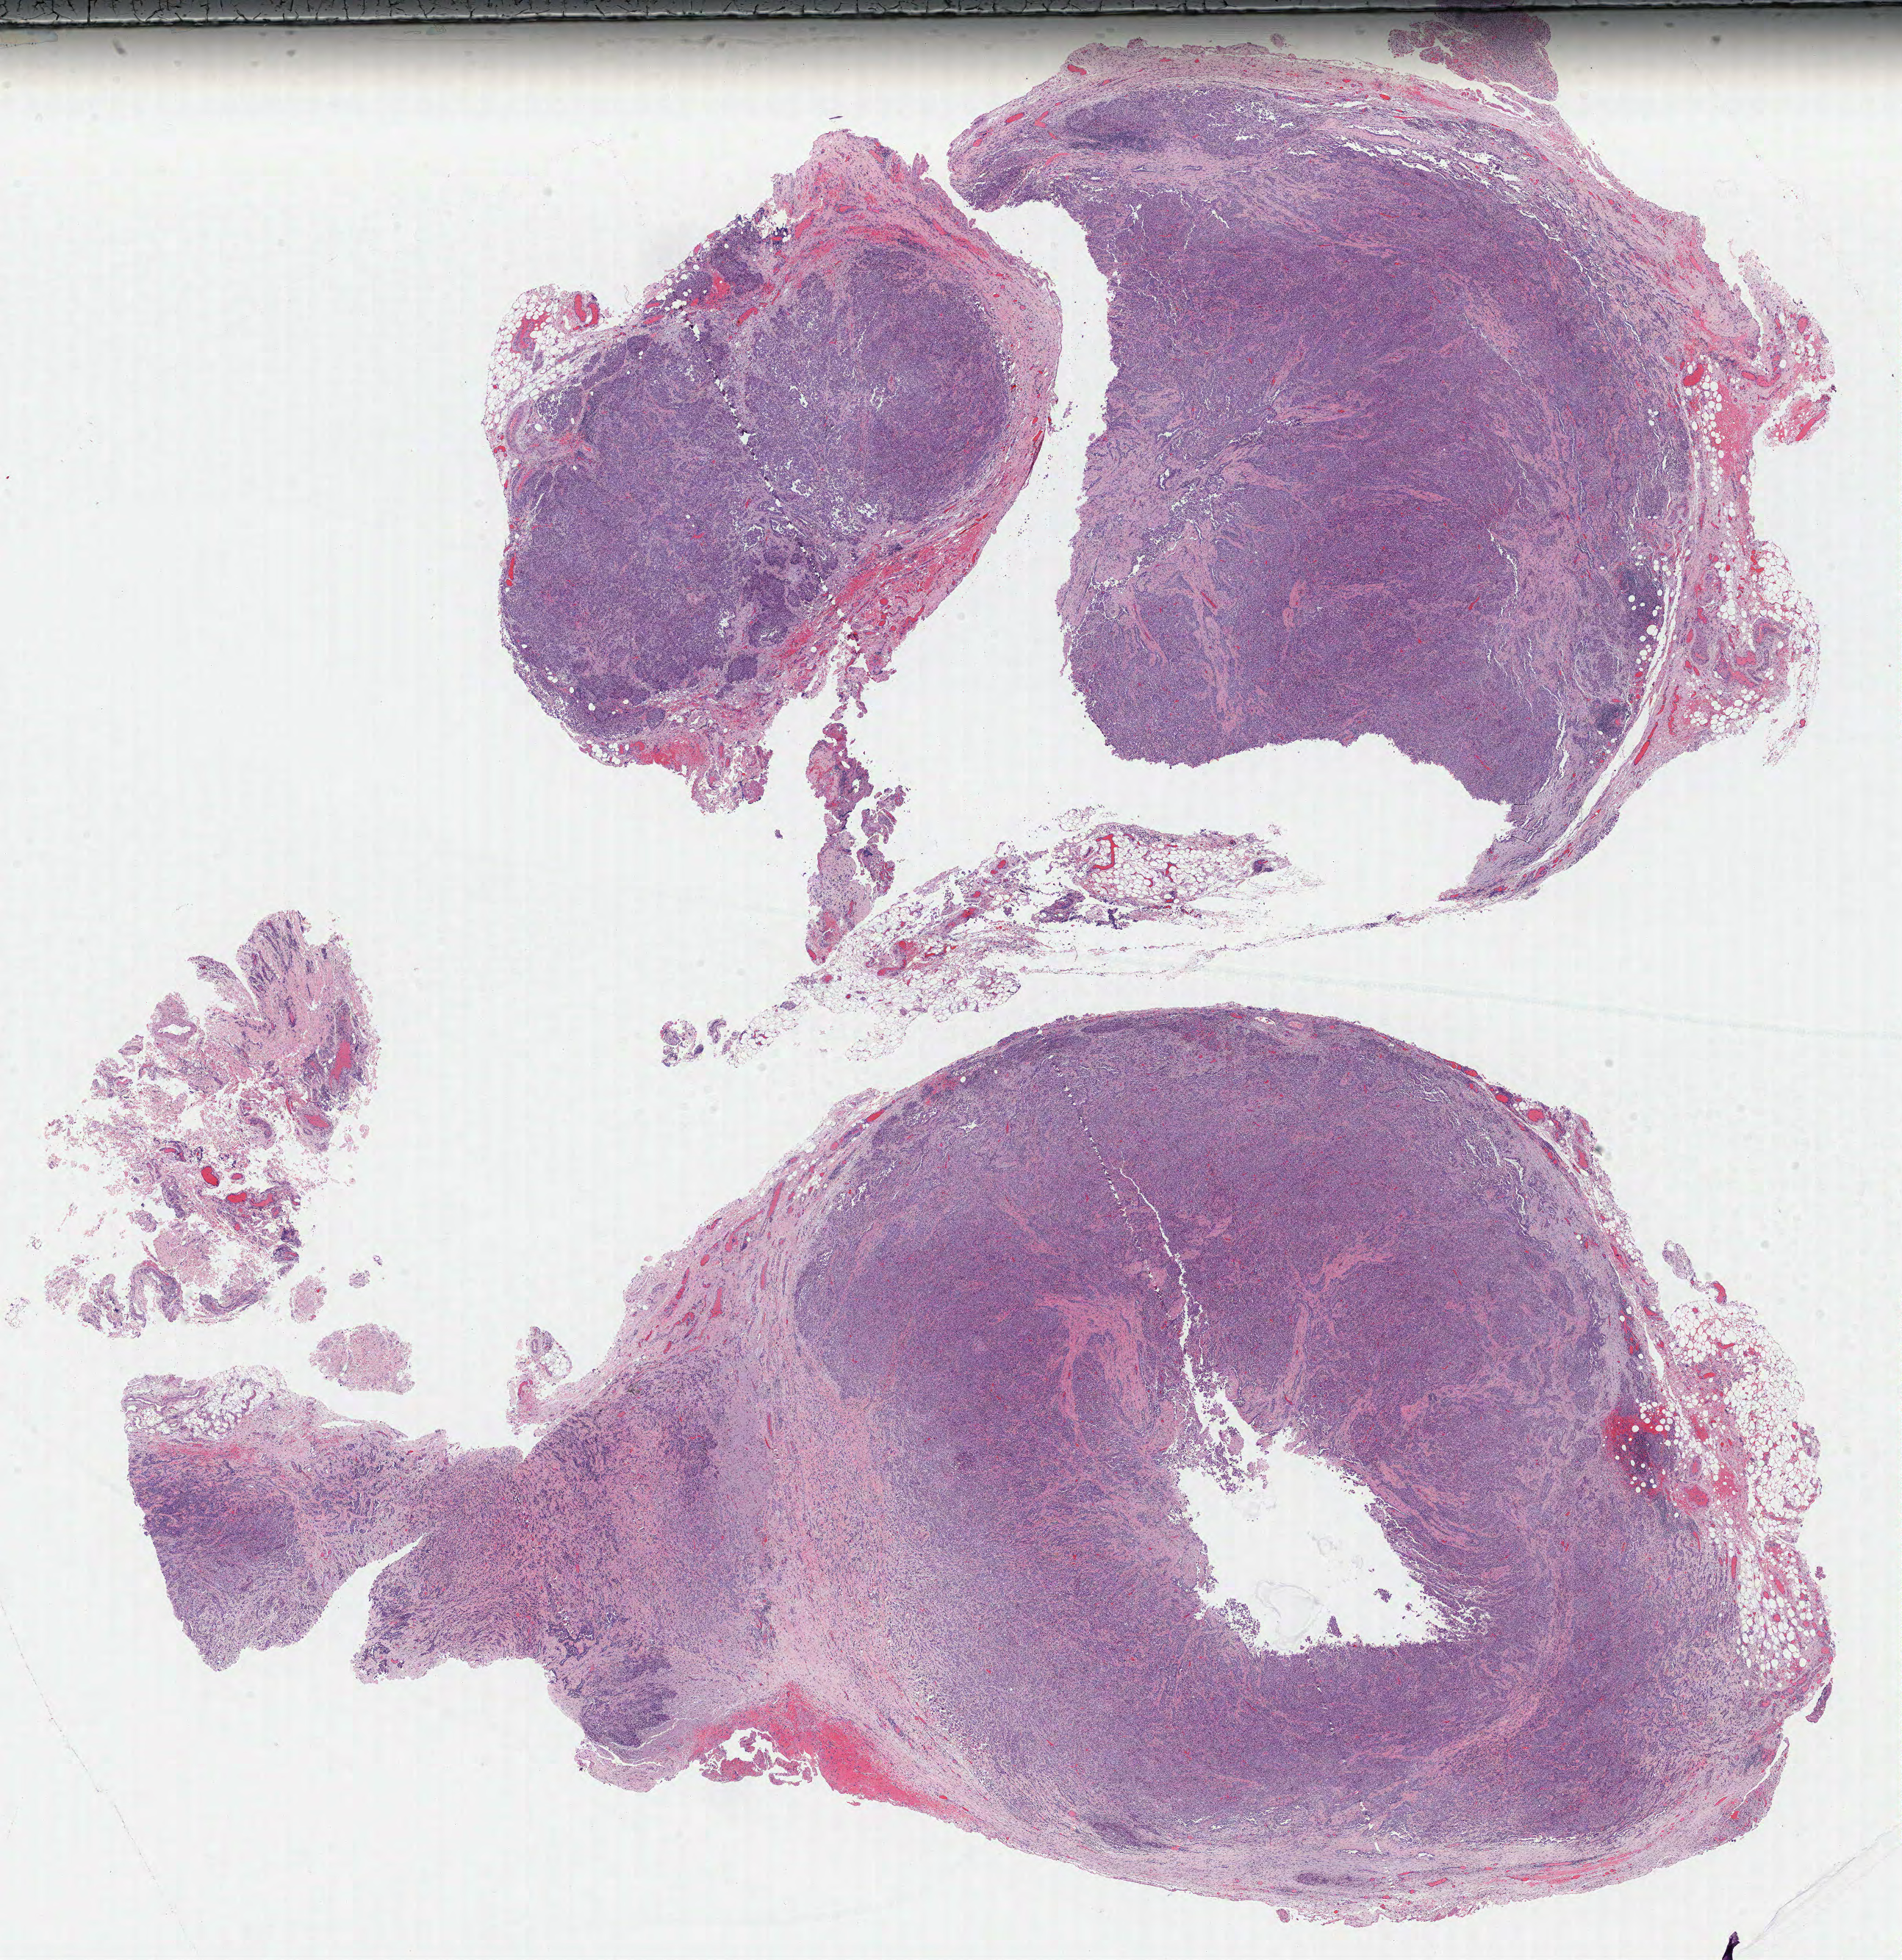
Whole-slide histology image, H&E-stained — a low-resolution overview of the entire scanned area, about 20.7 x 21.3 mm (slide scanned at 40x), formalin-fixed paraffin-embedded (FFPE) diagnostic section, sample: primary tumour, mesothelium. Male, age 57 years at initial diagnosis.
AJCC pathologic stage: IV (7th edition). TNM: T4 N2 M0. Pathologic diagnosis: Epithelioid mesothelioma, malignant.